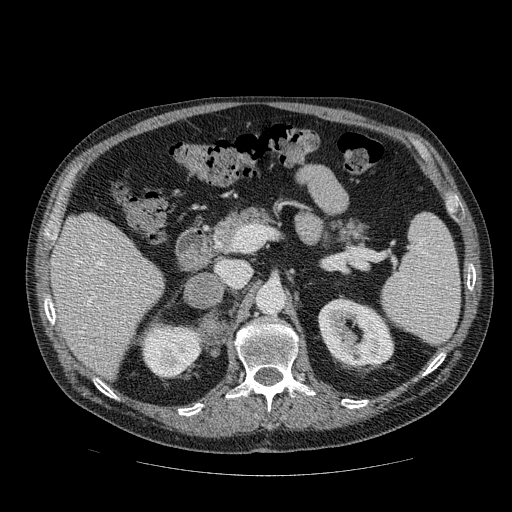
Contrast-enhanced abdominal CT, one axial slice. Position 49 of 111 along the scan axis. Reconstruction kernel STANDARD. Intravenous contrast given. Soft-tissue window (W 400 / L 40 HU). 2.5 mm slice thickness. 512 × 512 image matrix, field of view 420 × 420 mm. Male patient, age 56 years. Case-level facts recorded for this patient, not image findings: diagnosis: adrenocortical carcinoma; tumour side: right adrenal; tumour size at pathology: 9 cm; Ki-67 index: 48 %; stage (as recorded): 4.
Outlined on this slice (semi-automatically segmented with operator editing):
- mass: bounding box <185,273,223,340> (left, top, right, bottom; pixels)